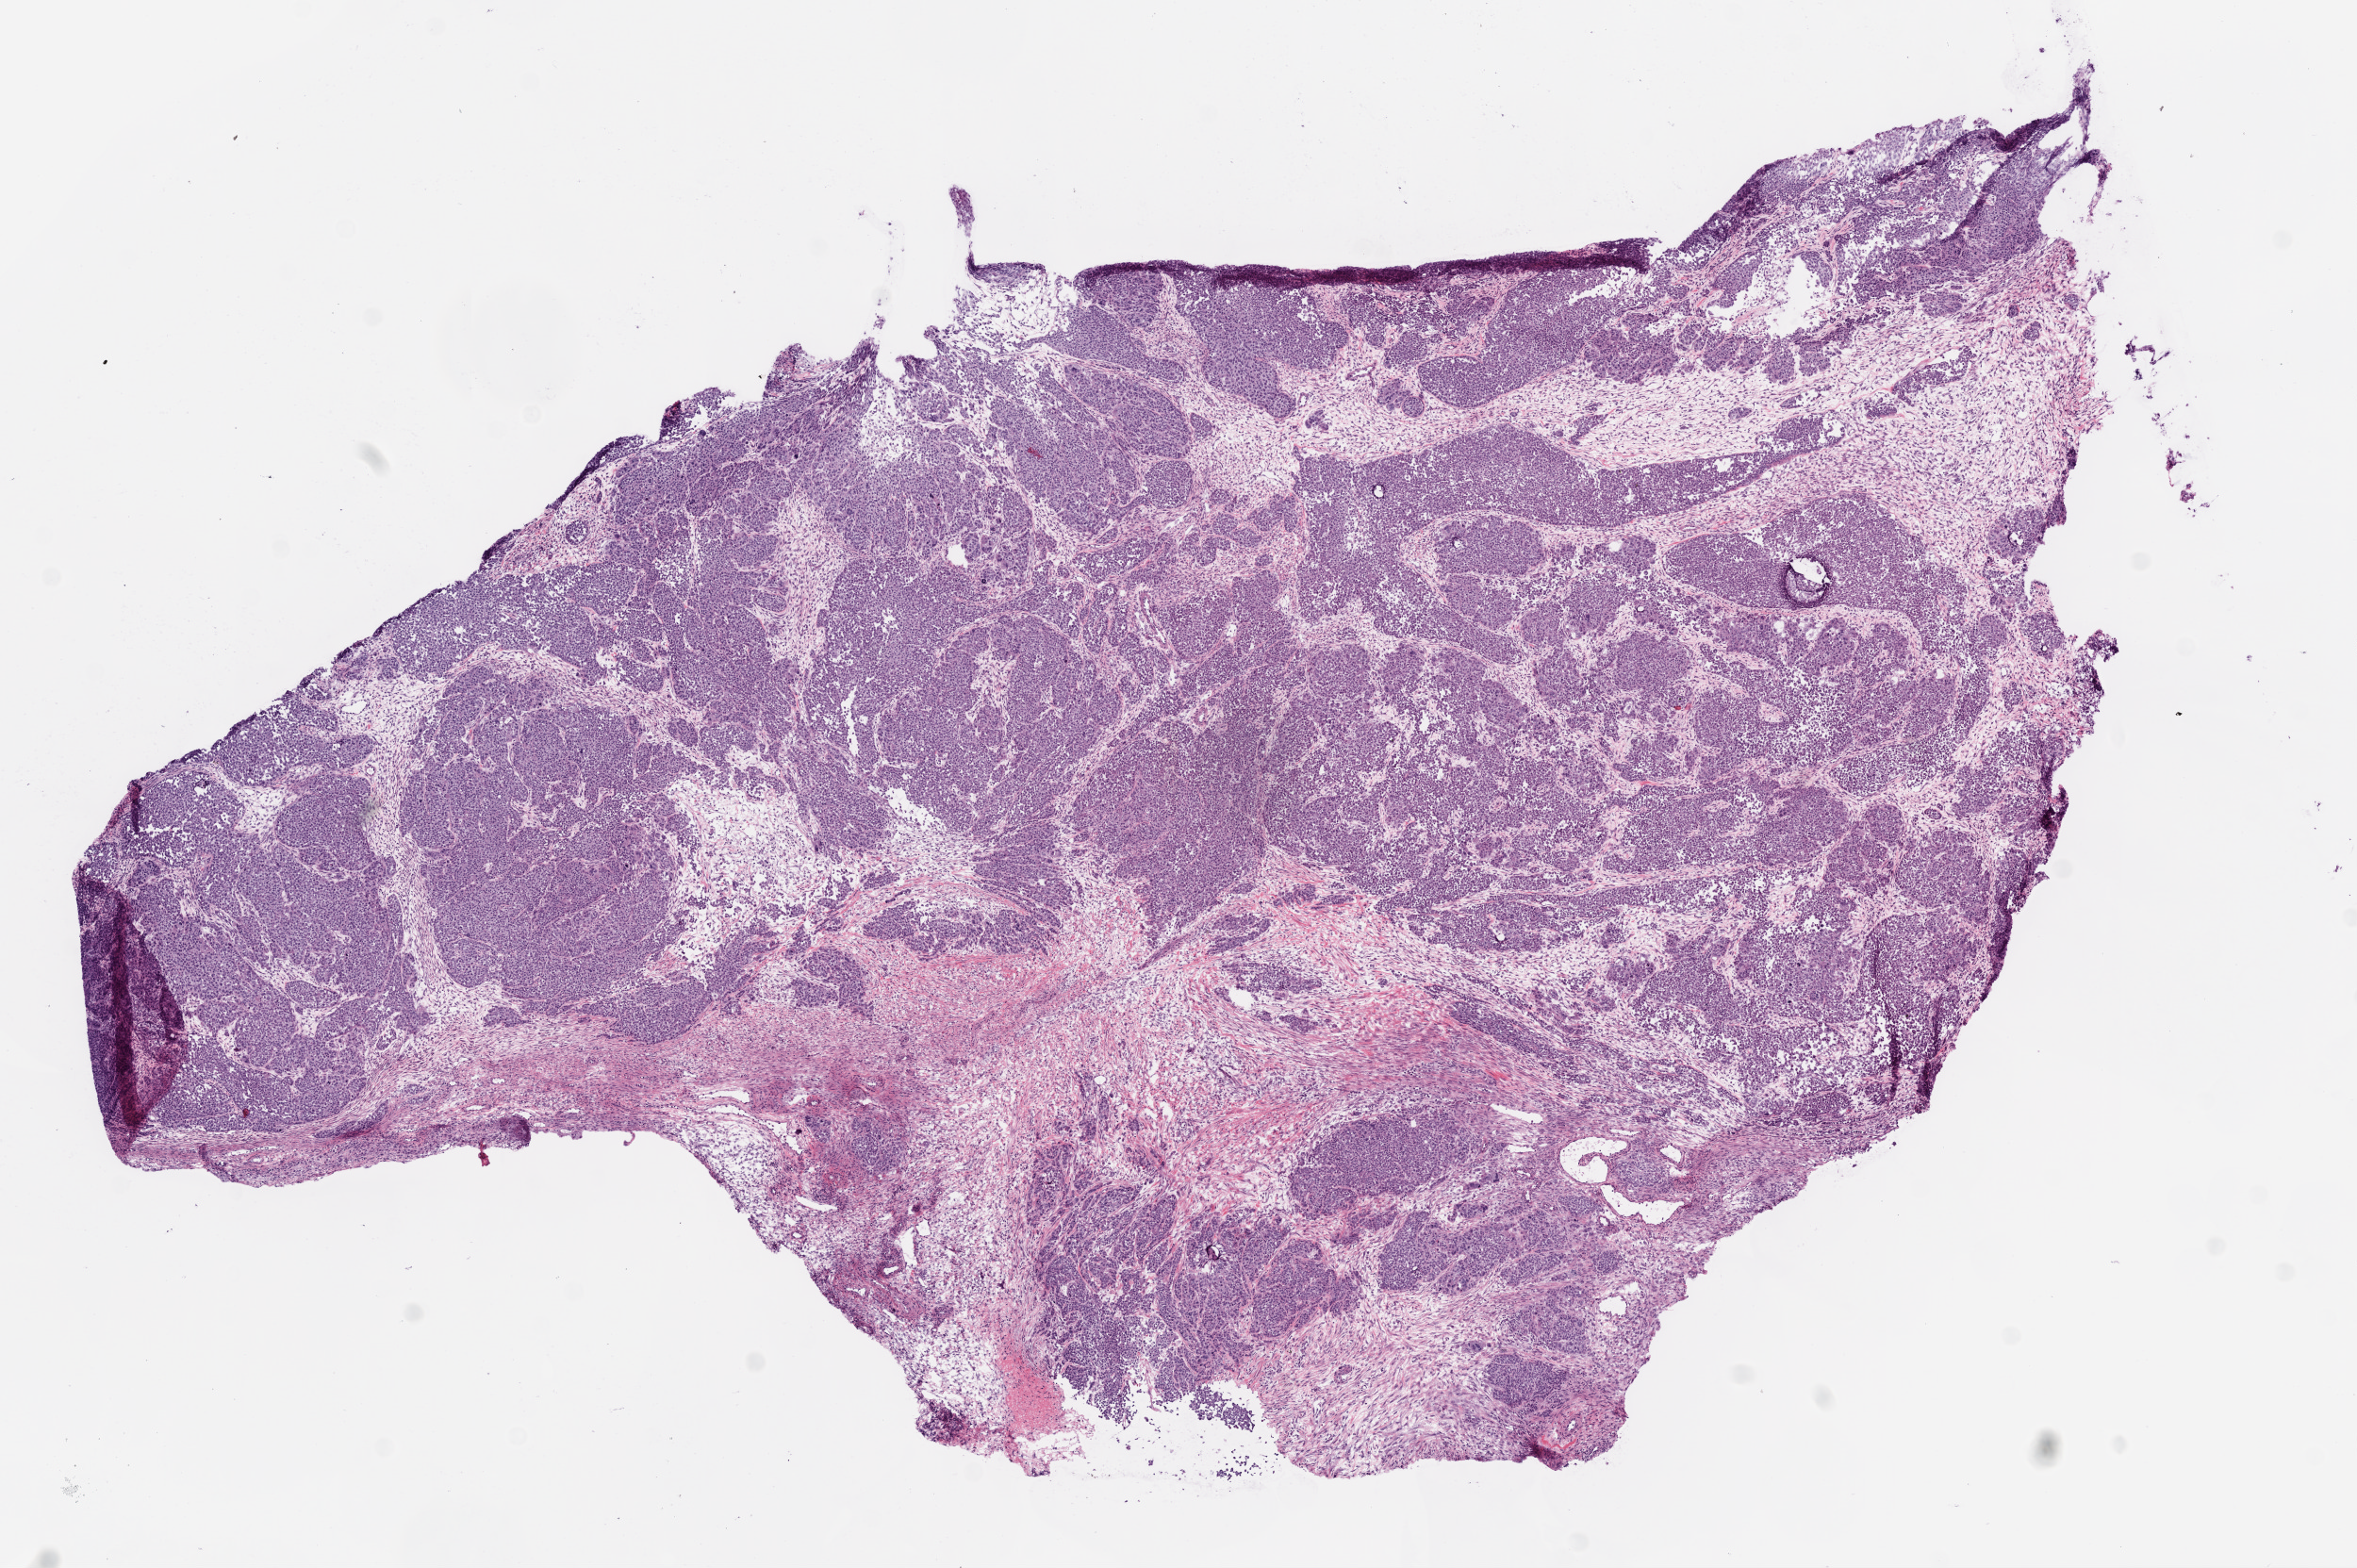
Hematoxylin and eosin (H&E) stained whole-slide image — low-resolution overview of the scanned area, about 10.0 x 6.7 mm. Frozen section from the bottom of the tissue portion. Primary tumour sample from the ovary. Patient: female, age at initial diagnosis 37 years. Histologic grade: G3 (poorly differentiated). Pathologist review of this section (percent, as recorded): tumour cells 75%, tumour nuclei 70%, normal cells 0%, stromal cells 25%, necrosis 5%.
- FIGO stage: IIIB
- histologic diagnosis: Serous cystadenocarcinoma, NOS